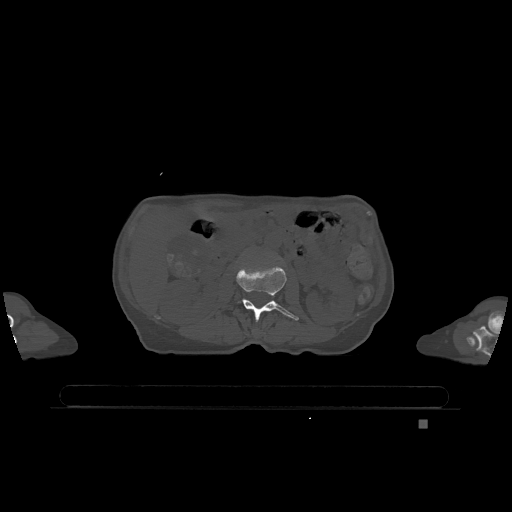
CT including the spine, one axial slice; slice 411 of 1317 in the series (ordered by position); bone window (W 1800 / L 400 HU); 512 × 512 image matrix, field of view 500 × 500 mm. Female patient, age 74 years. From the clinical record (not read from this slice): primary cancer: lung.
Outlined on this slice (semi-automatic segmentation, software-assisted and operator-edited):
- L2 vertebra: bounding box (x1, y1, x2, y2) in pixels: (236, 265, 299, 322)